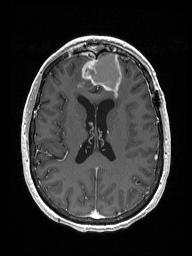
Brain MRI from a brain-tumour surgery series, one axial slice; slice 72 of 192 in the series (ordered by position); T1-weighted post-contrast; 1 mm slice thickness; 192 × 256 image matrix, field of view 187 × 250 mm. From the clinical record (not read from this slice): histopathology: Metastastic Carcinoma from Breast primary; tumour location: Right Frontal.
Outlined on this slice (manually delineated by an expert):
- previous resection cavity: bounding box <86,52,122,95> (left, top, right, bottom; pixels)